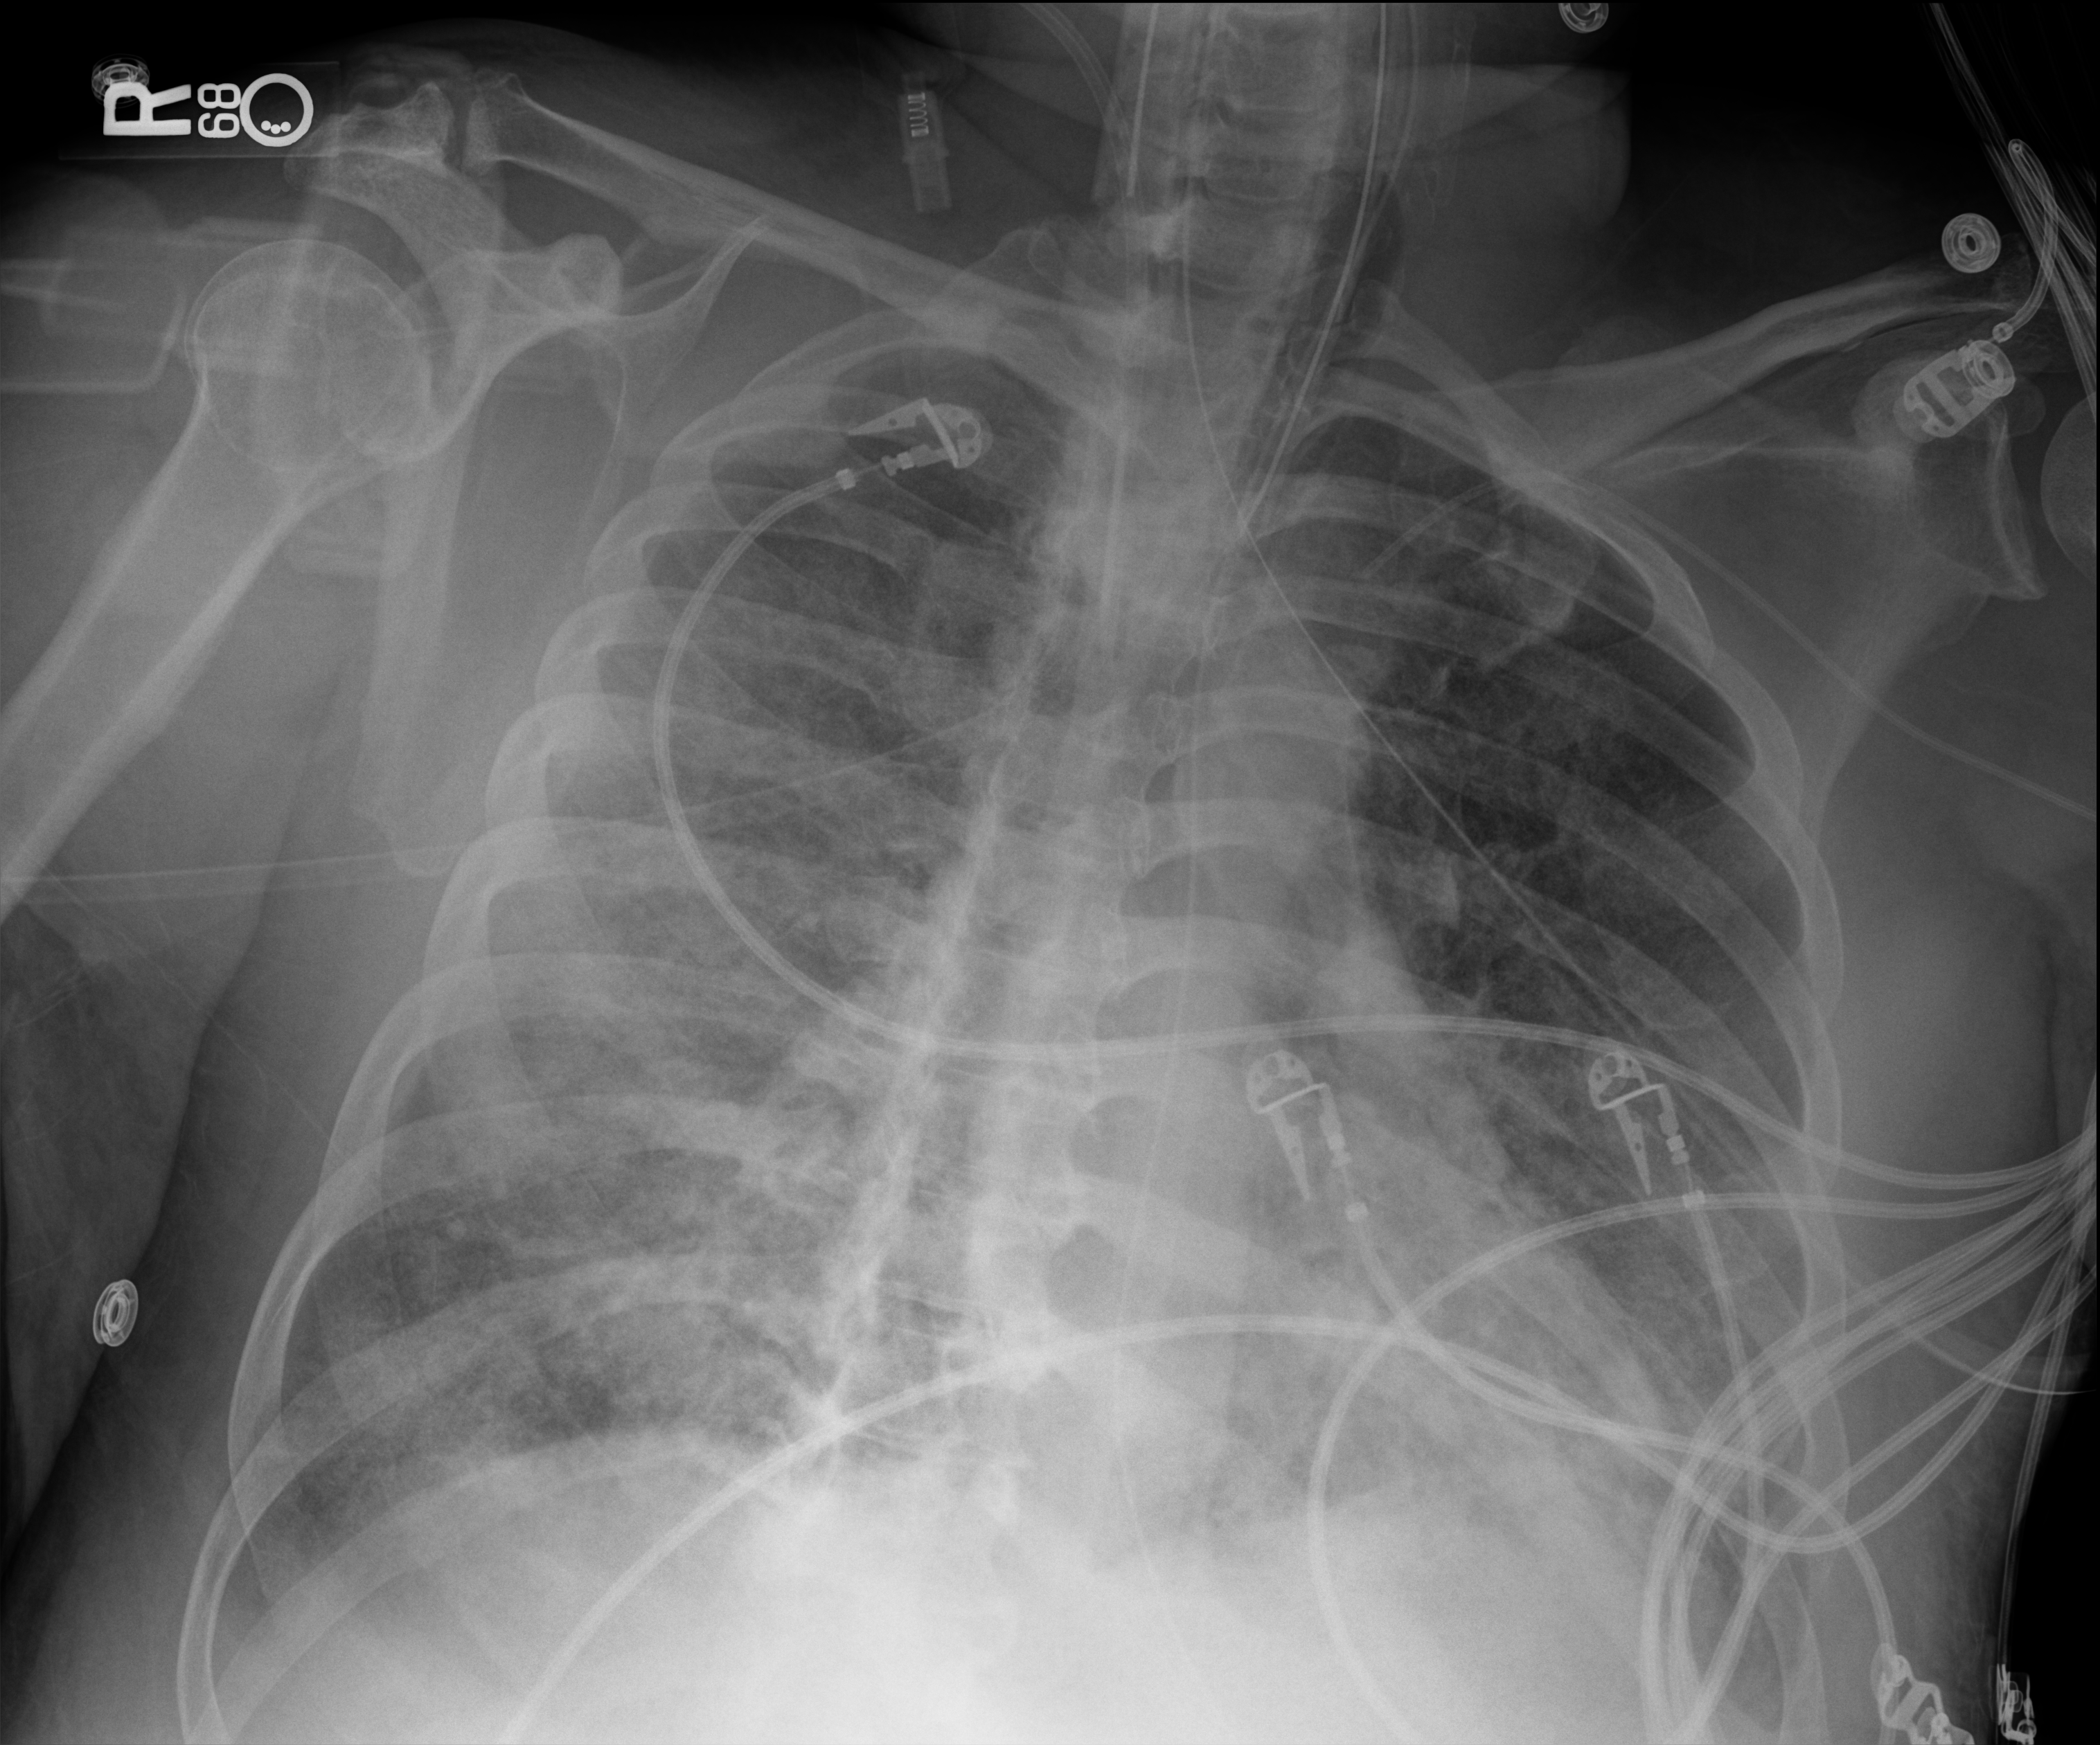
Bedside chest radiograph (digital radiography); anteroposterior (AP) projection. Male patient hospitalised with COVID-19, age 60–74 years.
Hospital-stay facts (about this admission, not read from this image; timing relative to this image not recorded): chronic kidney disease (admission record): no; mechanically ventilated during this hospital stay: yes.